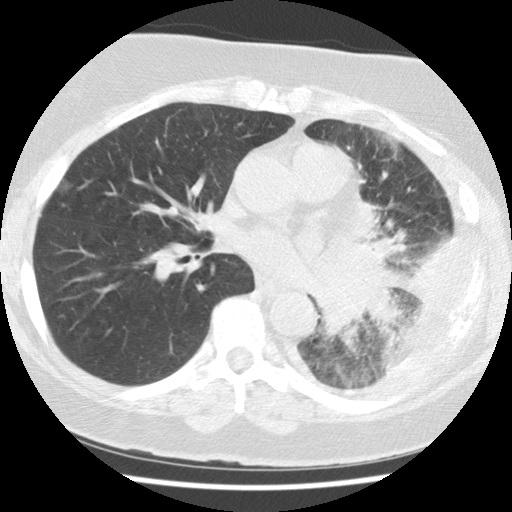
Low-dose screening chest CT, axial slice, baseline screening round, lung window (W 1500 / L -600 HU), standard (soft-tissue) reconstruction kernel (STANDARD), slice 59 of 114 in the series, 512 × 512 image matrix, field of view 320 × 320 mm. Female, age 65 years at enrolment. Current smoker at enrolment.
Expert reader's lesion annotation, bounding box <302,282,407,366> (left, top, right, bottom; pixels). Screening reader's record for this exam (one nodule recorded; not confirmed to be the boxed lesion): non-calcified nodule or mass ≥4 mm, left lower lobe, 74 × 48 mm, spiculated (stellate) margins, soft tissue attenuation. Official screen result: positive, change unspecified: nodule(s) >= 4 mm or enlarging nodule(s), mass(es), or other non-specific abnormalities suspicious for lung cancer. Lung cancer was diagnosed 13 days after this screen: adenocarcinoma, NOS, left lower lobe, stage IV (AJCC 6th edition), 74 mm at pathology.